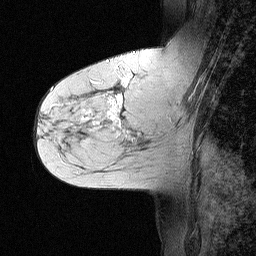
Breast MRI (dynamic contrast-enhanced), one sagittal slice; slice 26 of 64 in the series (ordered by position); dynamic contrast-enhanced study with each time point stored as its own series, time point 2 of 3 at this slice position (early post-contrast, ordered by acquisition time); 1.5 T; TE 4.5 ms, TR 11 ms; 256 × 256 image matrix, field of view 200 × 200 mm. Patient: female, 55 years. Case-level facts recorded for this patient, not image findings: setting: breast cancer imaged before/during neoadjuvant chemotherapy; receptor status: triple-negative.
Outlined on this slice (semi-automatically segmented with operator editing):
- analysis volume of interest (the breast-tissue region the enhancement analysis was run in; not a lesion): bounding box (x1, y1, x2, y2) in pixels: (71, 63, 147, 145)
- tumour enhancement mask (voxels above the 90 % enhancement threshold inside the analysis volume of interest): (82, 78, 128, 132)